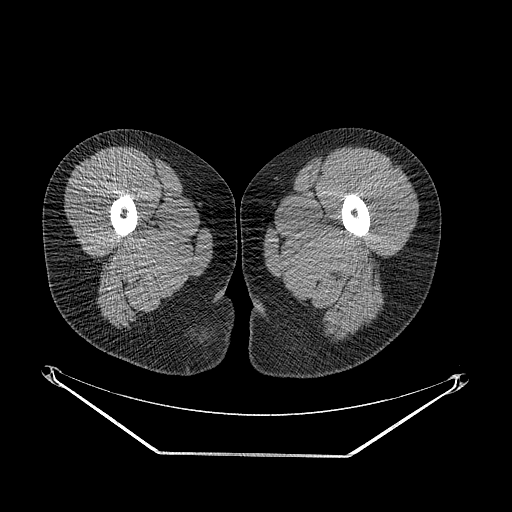
CT of an extremity soft-tissue mass (from a PET/CT study), one axial slice. Position 16 of 267 along the scan axis. 120 kVp. Soft-tissue window (W 400 / L 40 HU). 3.75 mm slice thickness. 512 × 512 image matrix, field of view 500 × 500 mm. Female patient. Case-level facts recorded for this patient, not image findings: histological type: epithelioid sarcoma; grade: intermediate; site of the primary tumour: right buttock.
Annotated regions visible in this slice (expert contour drawn on MRI and transferred to this co-registered scan by the dataset authors):
- gross tumour volume including surrounding oedema: bounding box [x1, y1, x2, y2] px = [185, 320, 232, 382]
- gross tumour volume (mass): [201, 331, 209, 343]